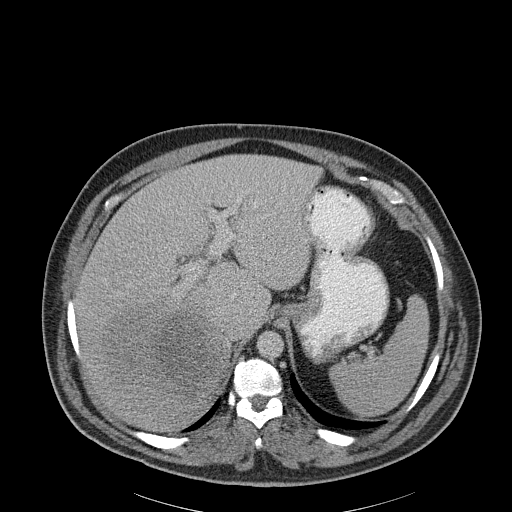
Contrast-enhanced abdominal CT, one axial slice. Position 148 of 186 along the scan axis. Reconstruction kernel B30f. Soft-tissue window (W 400 / L 40 HU). 3 mm slice thickness. 512 × 512 image matrix. Male patient, age 56 years. From the clinical record (not read from this slice): diagnosis: adrenocortical carcinoma; tumour side: right adrenal; tumour size at pathology: 18 cm; Ki-67 index: 2 %; stage (as recorded): 3.
Annotated regions visible in this slice (semi-automatic segmentation, software-assisted and operator-edited):
- mass: bounding box [x1, y1, x2, y2] px = [104, 306, 225, 402]